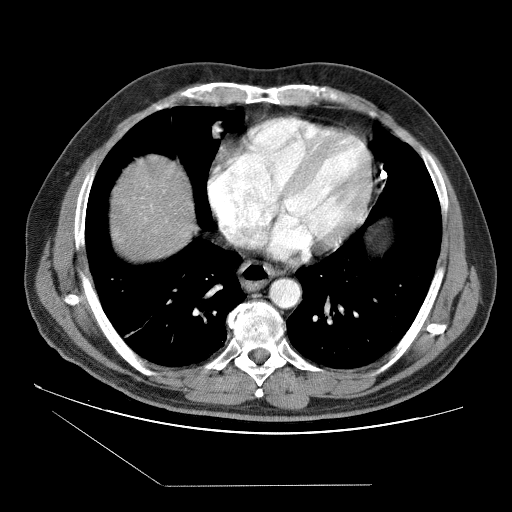
Contrast-enhanced abdominal CT (liver protocol), one axial slice; slice 81 of 87 in the series (ordered by position); 120 kVp; soft-tissue window (W 400 / L 40 HU); 512 × 512 image matrix, field of view 400 × 400 mm. Case-level facts recorded for this patient, not image findings: diagnosis: hepatocellular carcinoma (patient treated with transarterial chemoembolisation; whether this scan precedes or follows treatment is not stated here); TNM stage (as recorded): Stage-II; Child-Pugh class: B; tumour differentiation: no biopsy; tumour size: 2.6 cm.
Outlined on this slice (semi-automatic segmentation, software-assisted and operator-edited):
- liver parenchyma outside the tumour (the mass and vessels are separate outlines, so this box may not span the whole liver): bounding box (x1, y1, x2, y2) in pixels: (110, 154, 194, 258)